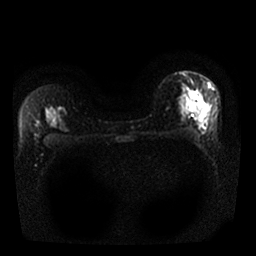
Breast MRI, one axial slice; position 17 of 25 along the scan axis; diffusion-weighted series; image 2 of 4 stored at this slice position (different b-values; order by instance number); 1.5 T; 256 × 256 image matrix, field of view 320 × 320 mm. Female patient.
Annotated regions visible in this slice (expert manual segmentation):
- tumour on diffusion-weighted imaging: bounding box (x1, y1, x2, y2) in pixels: (194, 94, 200, 103)